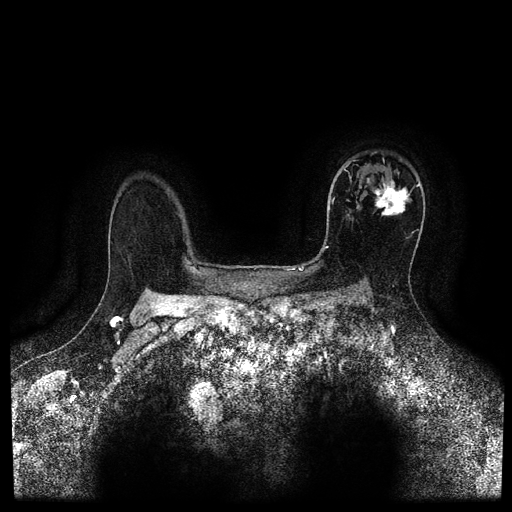
Breast MRI (dynamic contrast-enhanced, multi-phase), one axial slice; position 74 of 116 along the scan axis; dynamic contrast-enhanced series, time point 2 of 5 at this slice position (early post-contrast); 1.5 T; TE 2.7 ms, TR 5.4 ms; 512 × 512 image matrix, field of view 340 × 340 mm. Patient: female, 50 years.
Outlined on this slice (semi-automatic segmentation, software-assisted and operator-edited):
- breast lesion (labelled 'tumour' in the annotation; benign lesions carry a separate 'benign' label): bounding box (x1, y1, x2, y2) in pixels: (366, 175, 412, 218)